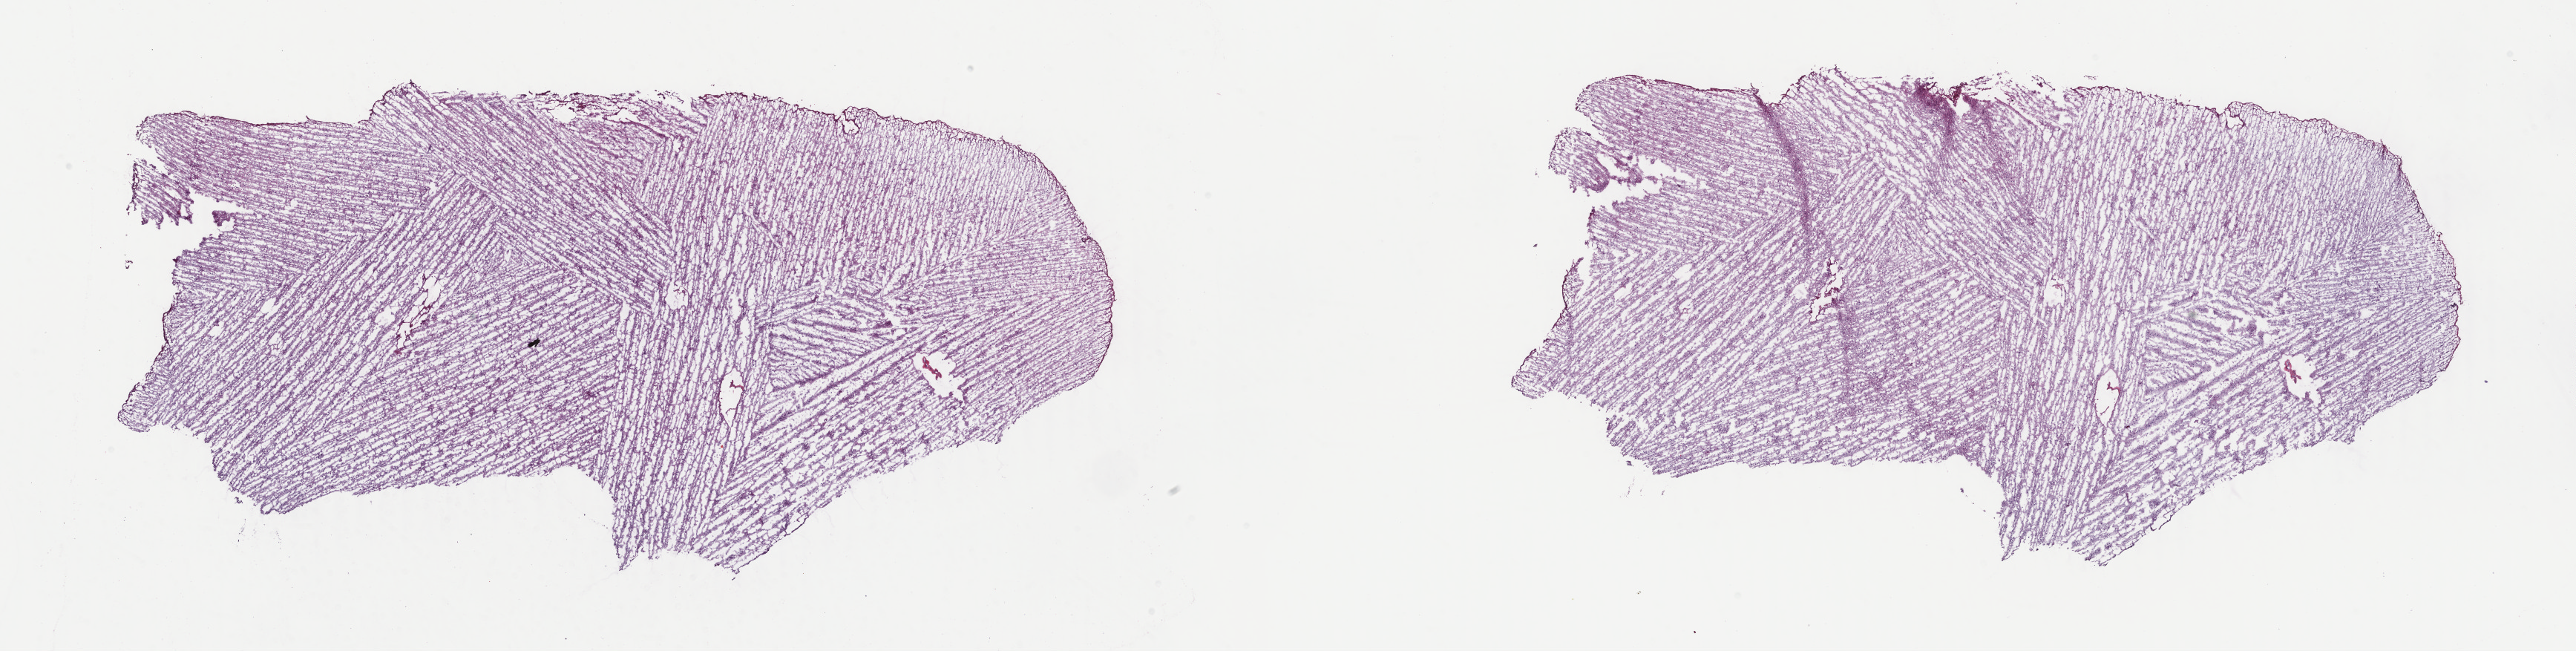
Whole-slide histology image, H&E-stained, shown as a low-resolution overview of the whole scanned area (about 27.6 x 7.0 mm, acquisition: 40x scan); frozen section from the top of the tissue portion; sample: primary tumour, brain. Male patient; age at initial diagnosis 39 years. Histologic grade: G2 (moderately differentiated). Slide review estimates, as recorded: tumour cells 45%, tumour nuclei 85%, normal cells 15%, stromal cells 40%, necrosis 0%. Infiltration values recorded for this section: lymphocyte infiltration 0%, monocyte infiltration 0%, neutrophil infiltration 0%.
Histologic diagnosis: Astrocytoma, NOS (cerebrum).